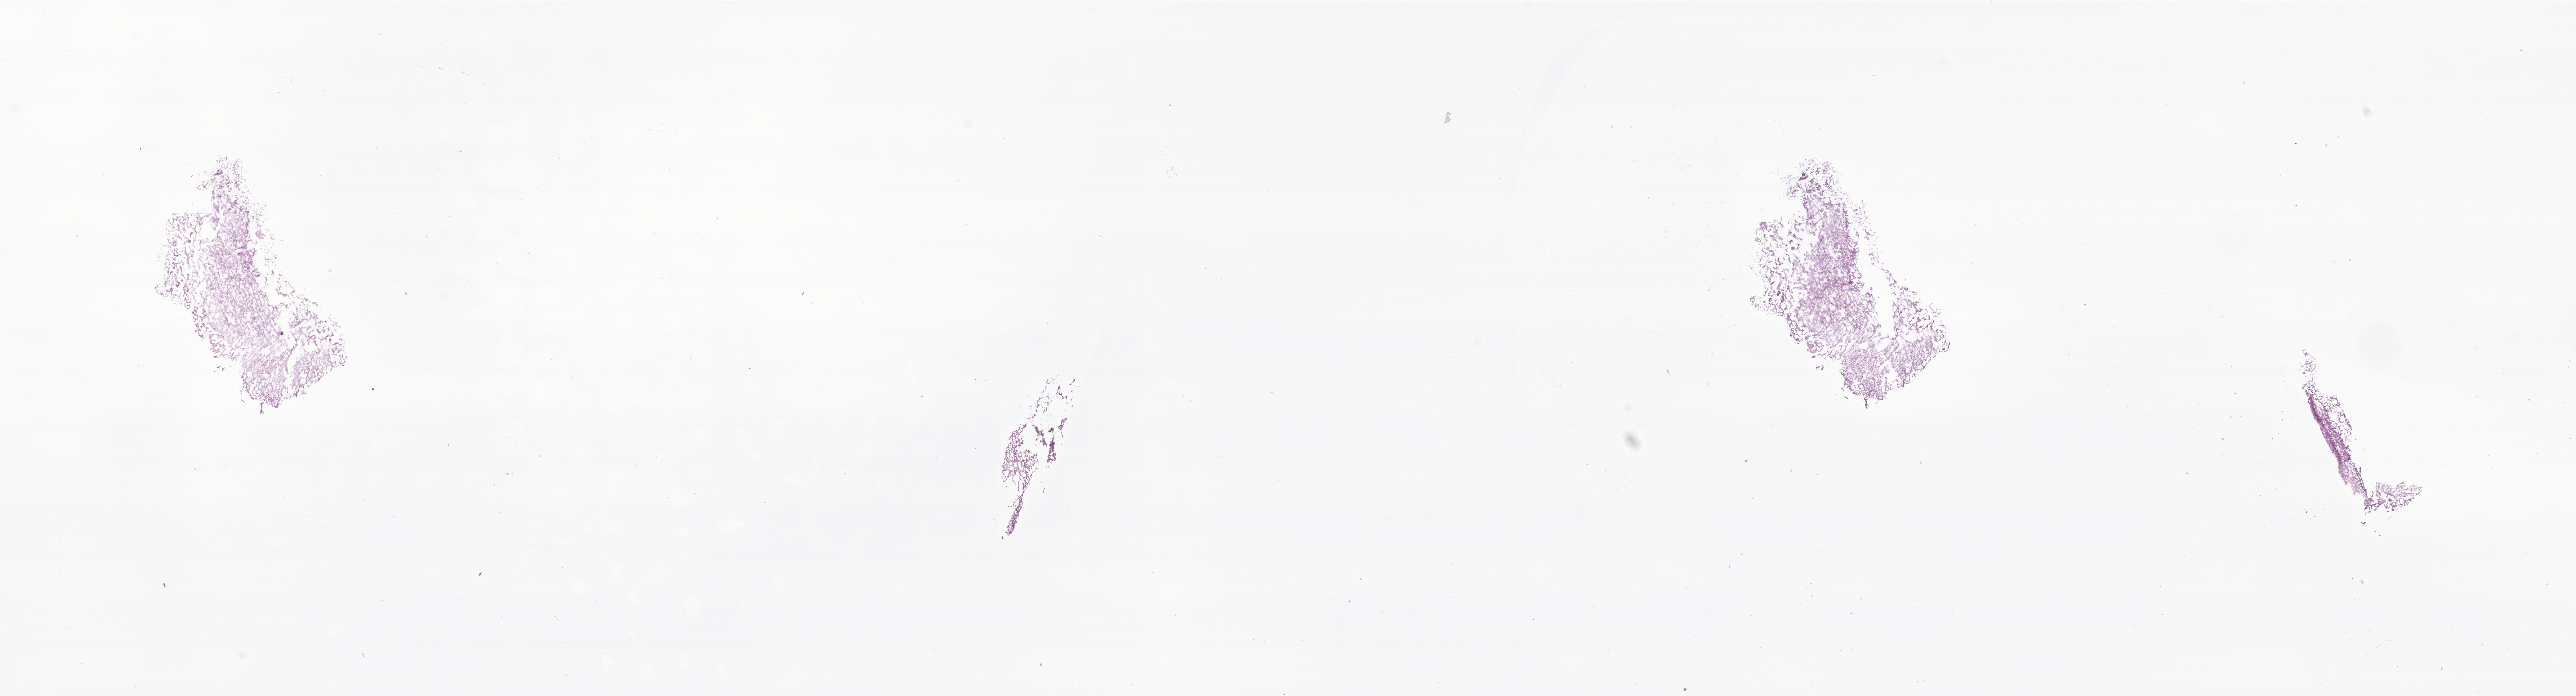
Whole-slide image, hematoxylin and eosin (H&E) stain of tumor tissue from the brain — whole scanned area (about 30.1 x 8.1 mm) shown as a low-resolution overview, frozen section (OCT-embedded). Patient: female, age 81 months.
Diagnosis: Pilocytic astrocytoma.